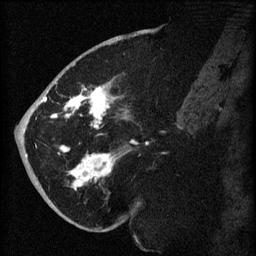
Breast MRI (dynamic contrast-enhanced), one sagittal slice; slice 32 of 60 in the series (ordered by position); dynamic contrast-enhanced series, image 2 of 3 at this slice position (ordered by acquisition); 1.5 T; TE 4.2 ms, TR 8.2 ms; 256 × 256 image matrix, field of view 180 × 180 mm. Female patient, age 71 years.
Outlined on this slice (semi-automatically segmented with operator editing):
- analysis volume of interest (the breast-tissue region the enhancement analysis was run in; not a lesion): box from (x=40, y=72) to (x=148, y=196) px
- tumour enhancement mask (voxels above the 70 % enhancement threshold inside the analysis volume of interest): (x=40, y=85)–(x=137, y=190)